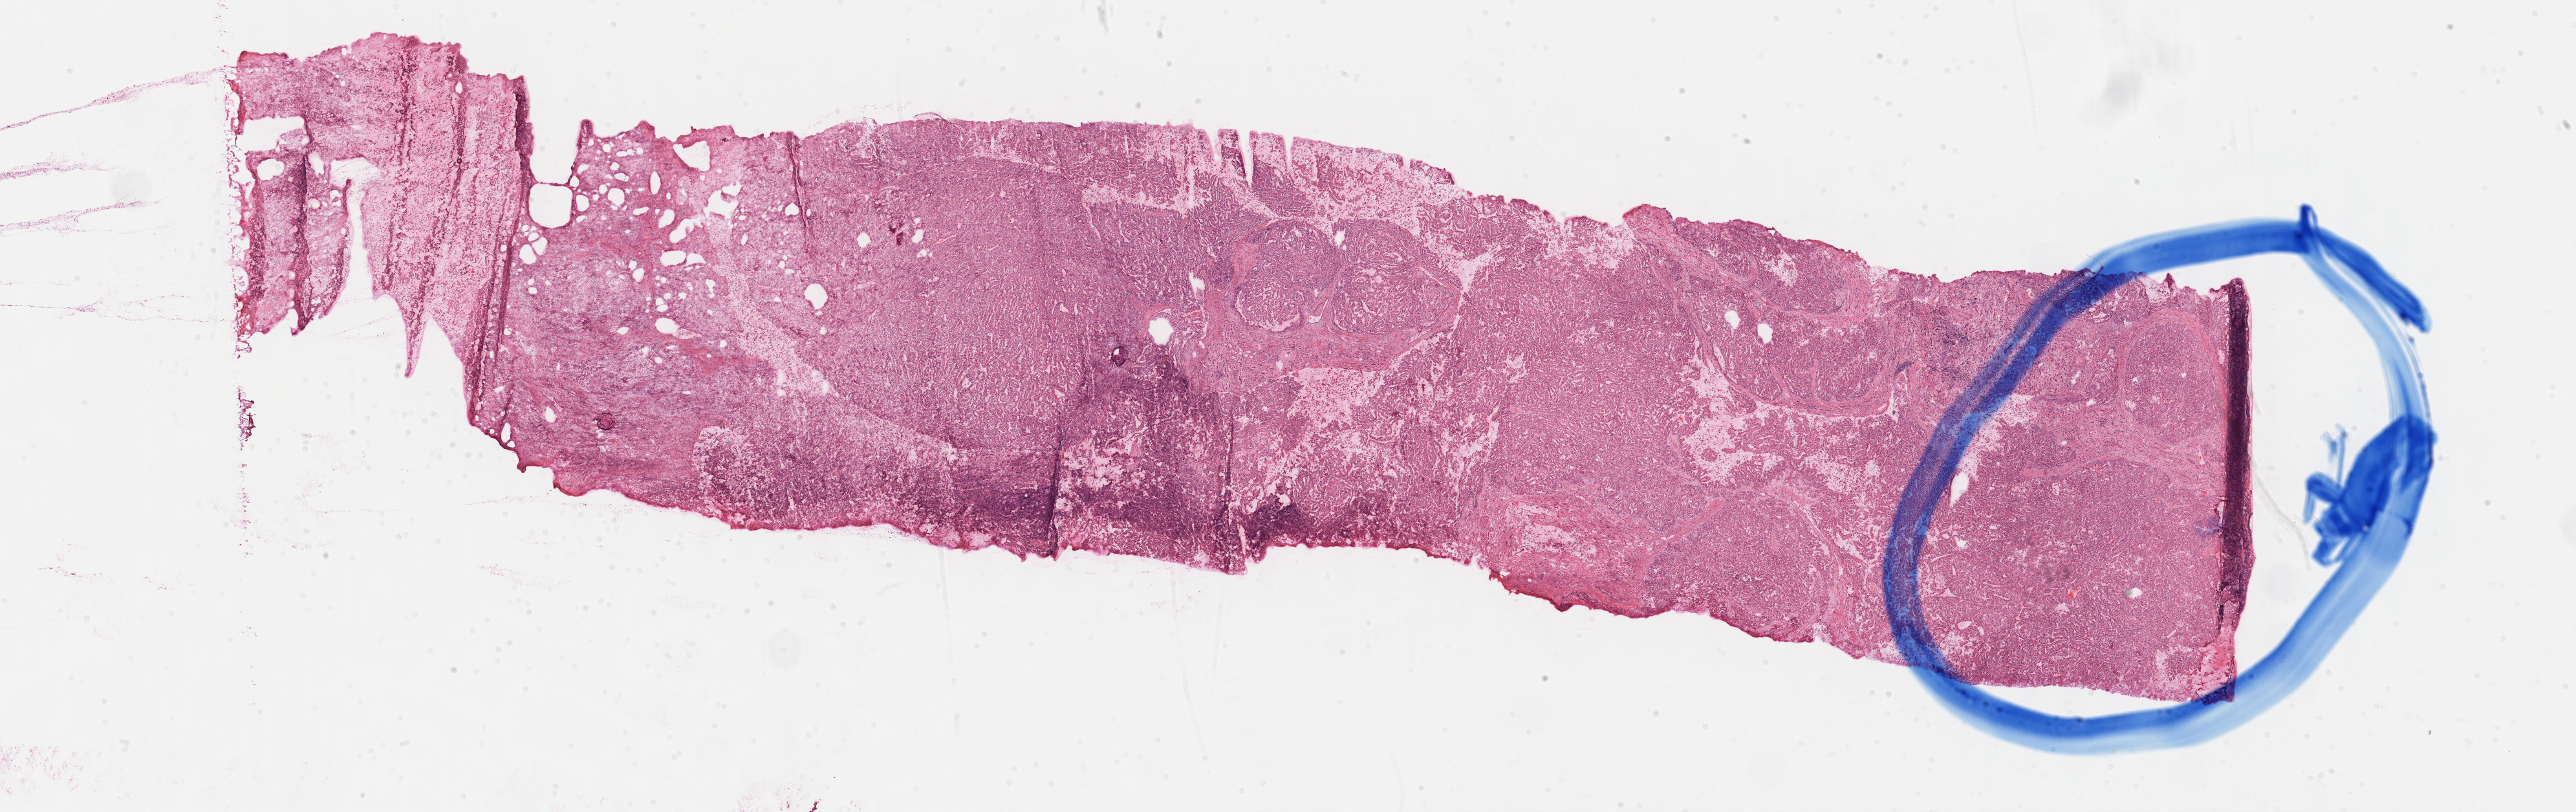
Whole-slide histology image, H&E, shown as a low-resolution overview of the whole scanned area (about 32.2 x 10.2 mm), formalin-fixed paraffin-embedded (FFPE) diagnostic section, sample: primary tumour, kidney. Female patient; age at initial diagnosis 65 years. Histologic grade: G4 (undifferentiated).
AJCC pathologic stage: IV. TNM: T3a NX M1. Pathologic diagnosis: Clear cell adenocarcinoma, NOS.